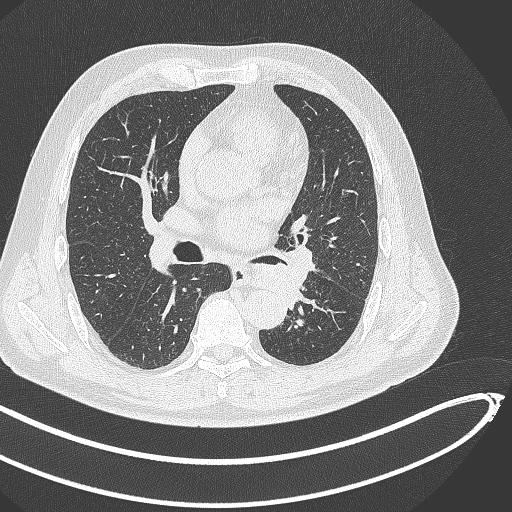
Chest CT, one axial slice; reconstruction kernel B70f; lung window (W 1500 / L -600 HU); 1 mm slice thickness; 512 × 512 image matrix. Patient: male, 64 years. From the clinical record (not read from this slice): clinical TNM (as recorded): T1c N0 M0; histopathological grade: G2.
Annotated regions visible in this slice (rectangle marked by the reading radiologist):
- lung tumour (recorded histology: squamous cell carcinoma): bounding box (x1, y1, x2, y2) in pixels: (251, 261, 309, 315)